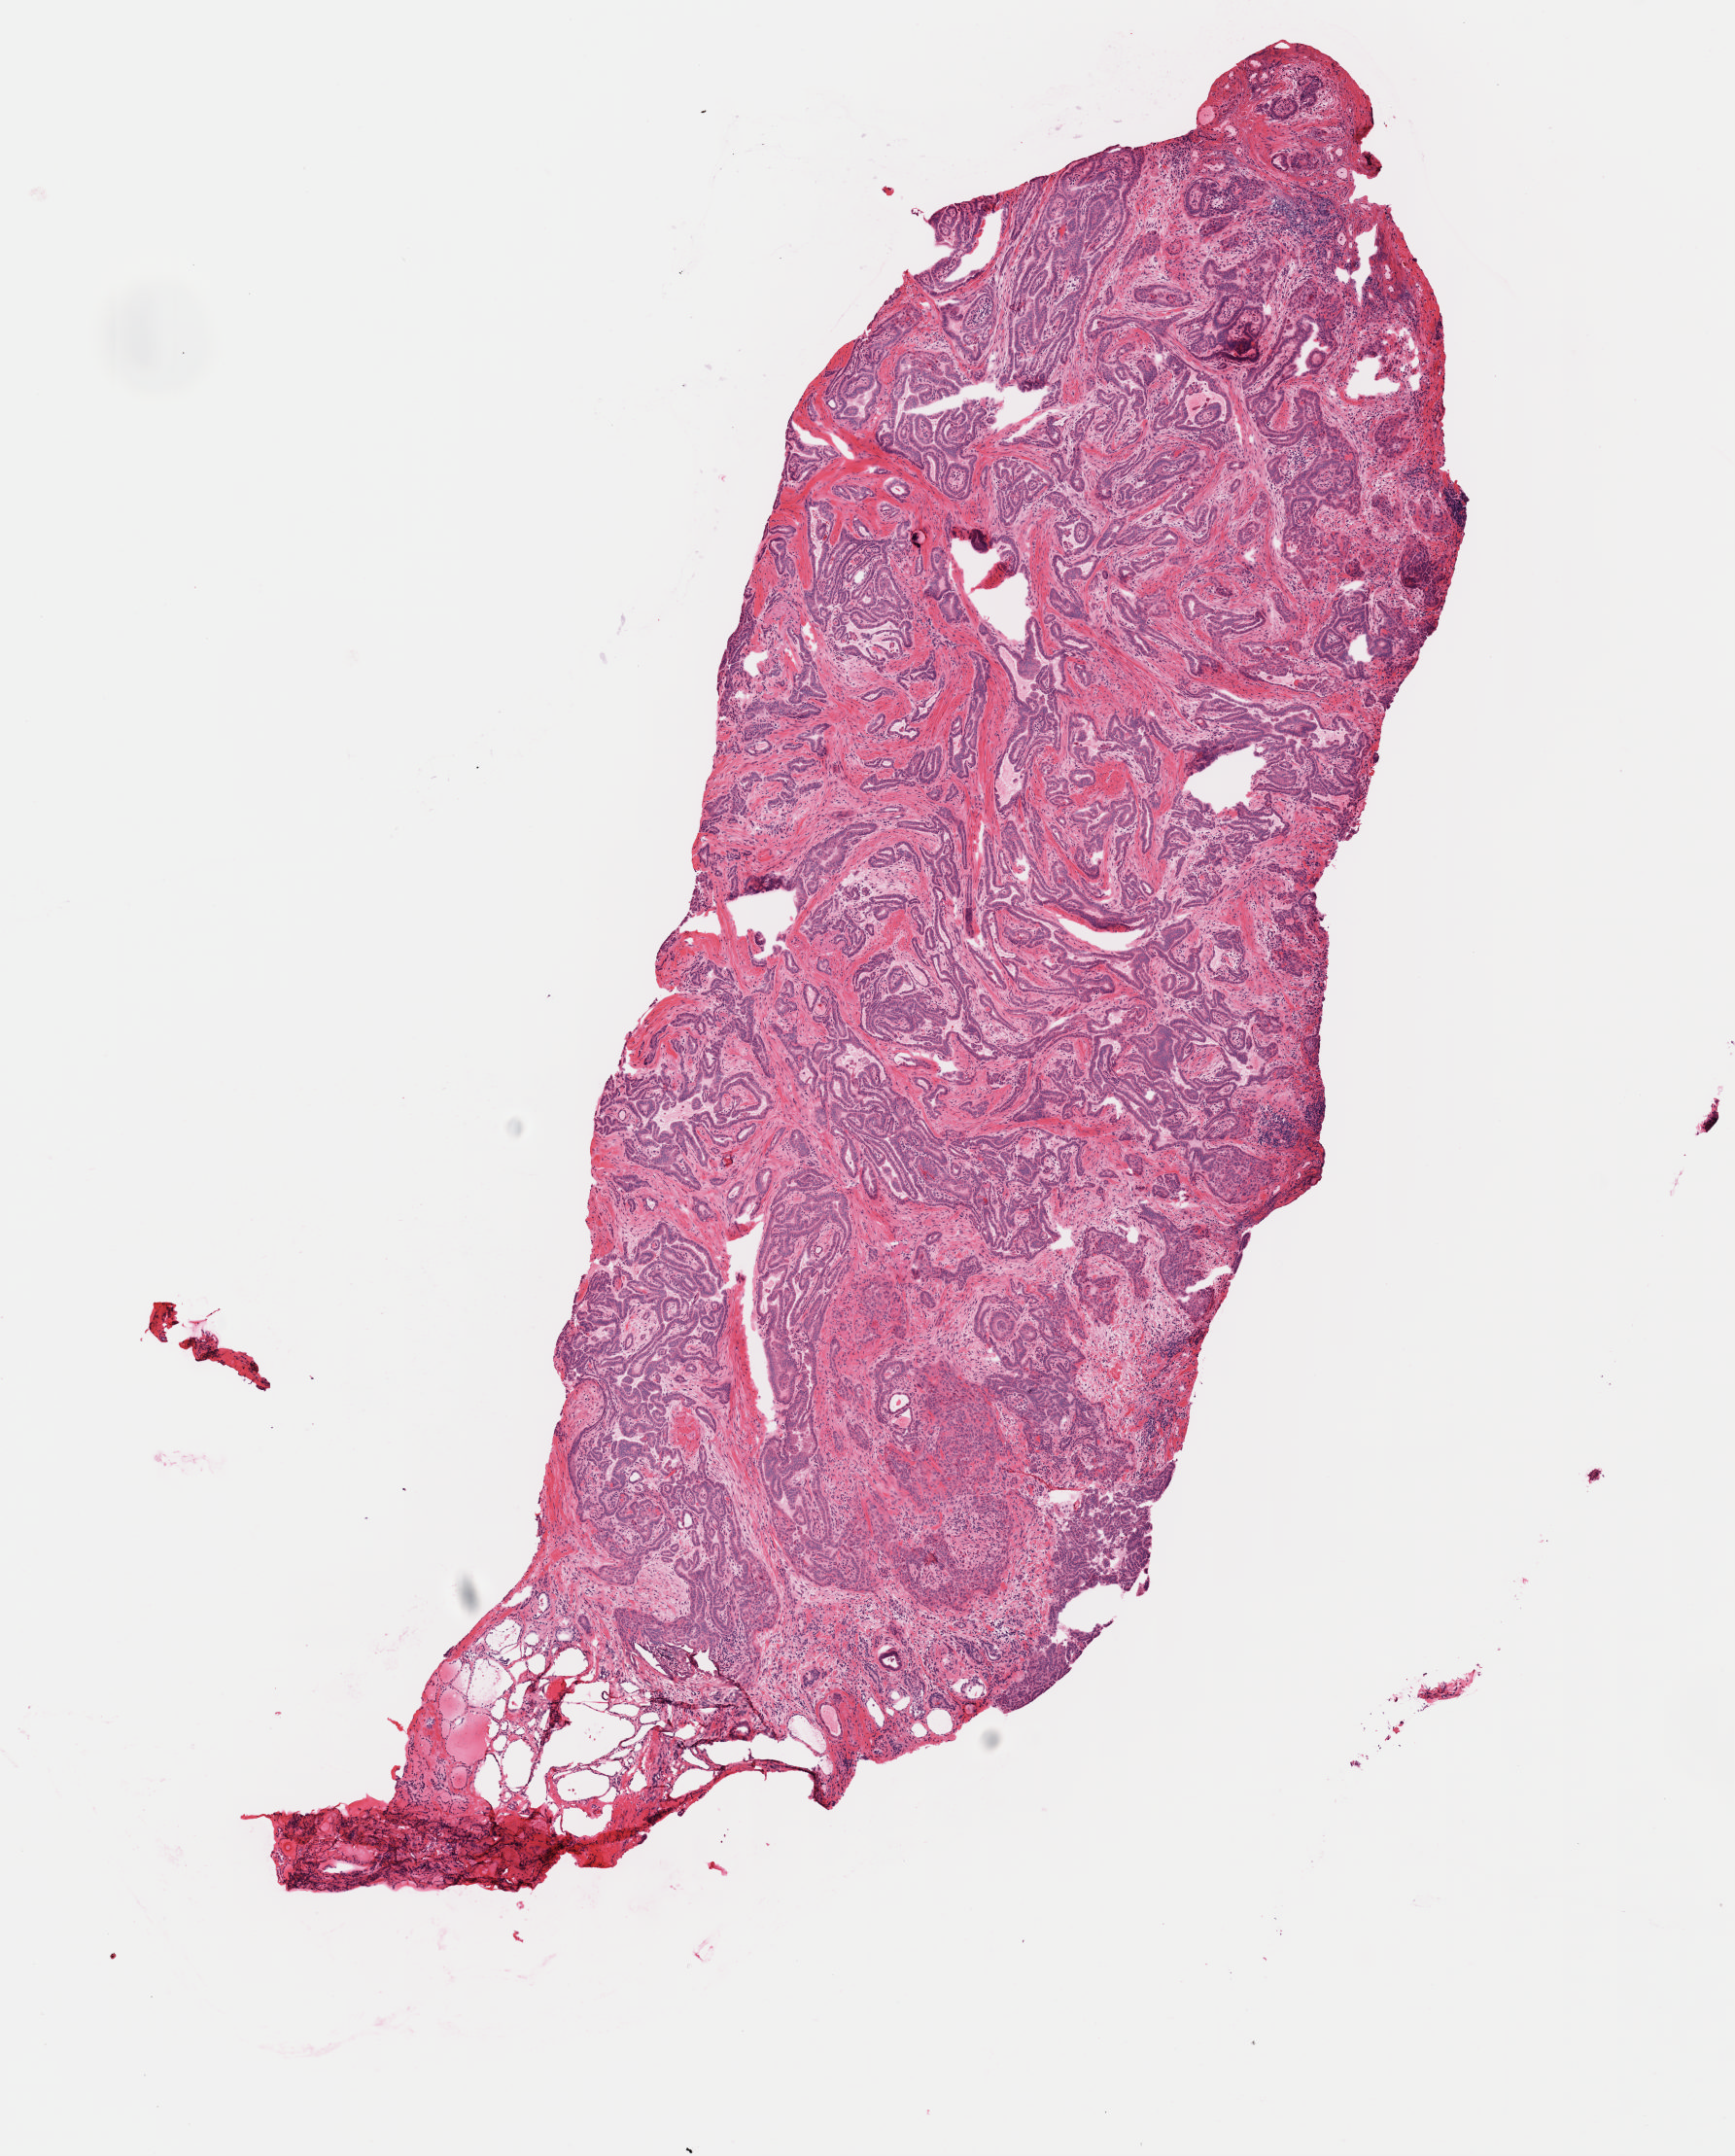
H&E whole-slide image, a low-resolution overview of the entire scanned area, about 7.0 x 8.8 mm (acquisition: 40x scan), frozen section from the top of the tissue portion, primary tumour sample from the thyroid. Patient: female, age at initial diagnosis 45 years. Pathologist review of this section (percent, as recorded): tumour cells 85%, tumour nuclei 85%, normal cells 2%, stromal cells 13%, necrosis 0%. Inflammatory infiltration, as recorded: lymphocyte infiltration 2%, monocyte infiltration 1%, neutrophil infiltration 0%.
Laterality: left. Diagnosis: Papillary carcinoma, columnar cell (thyroid gland). AJCC pathologic stage: III.